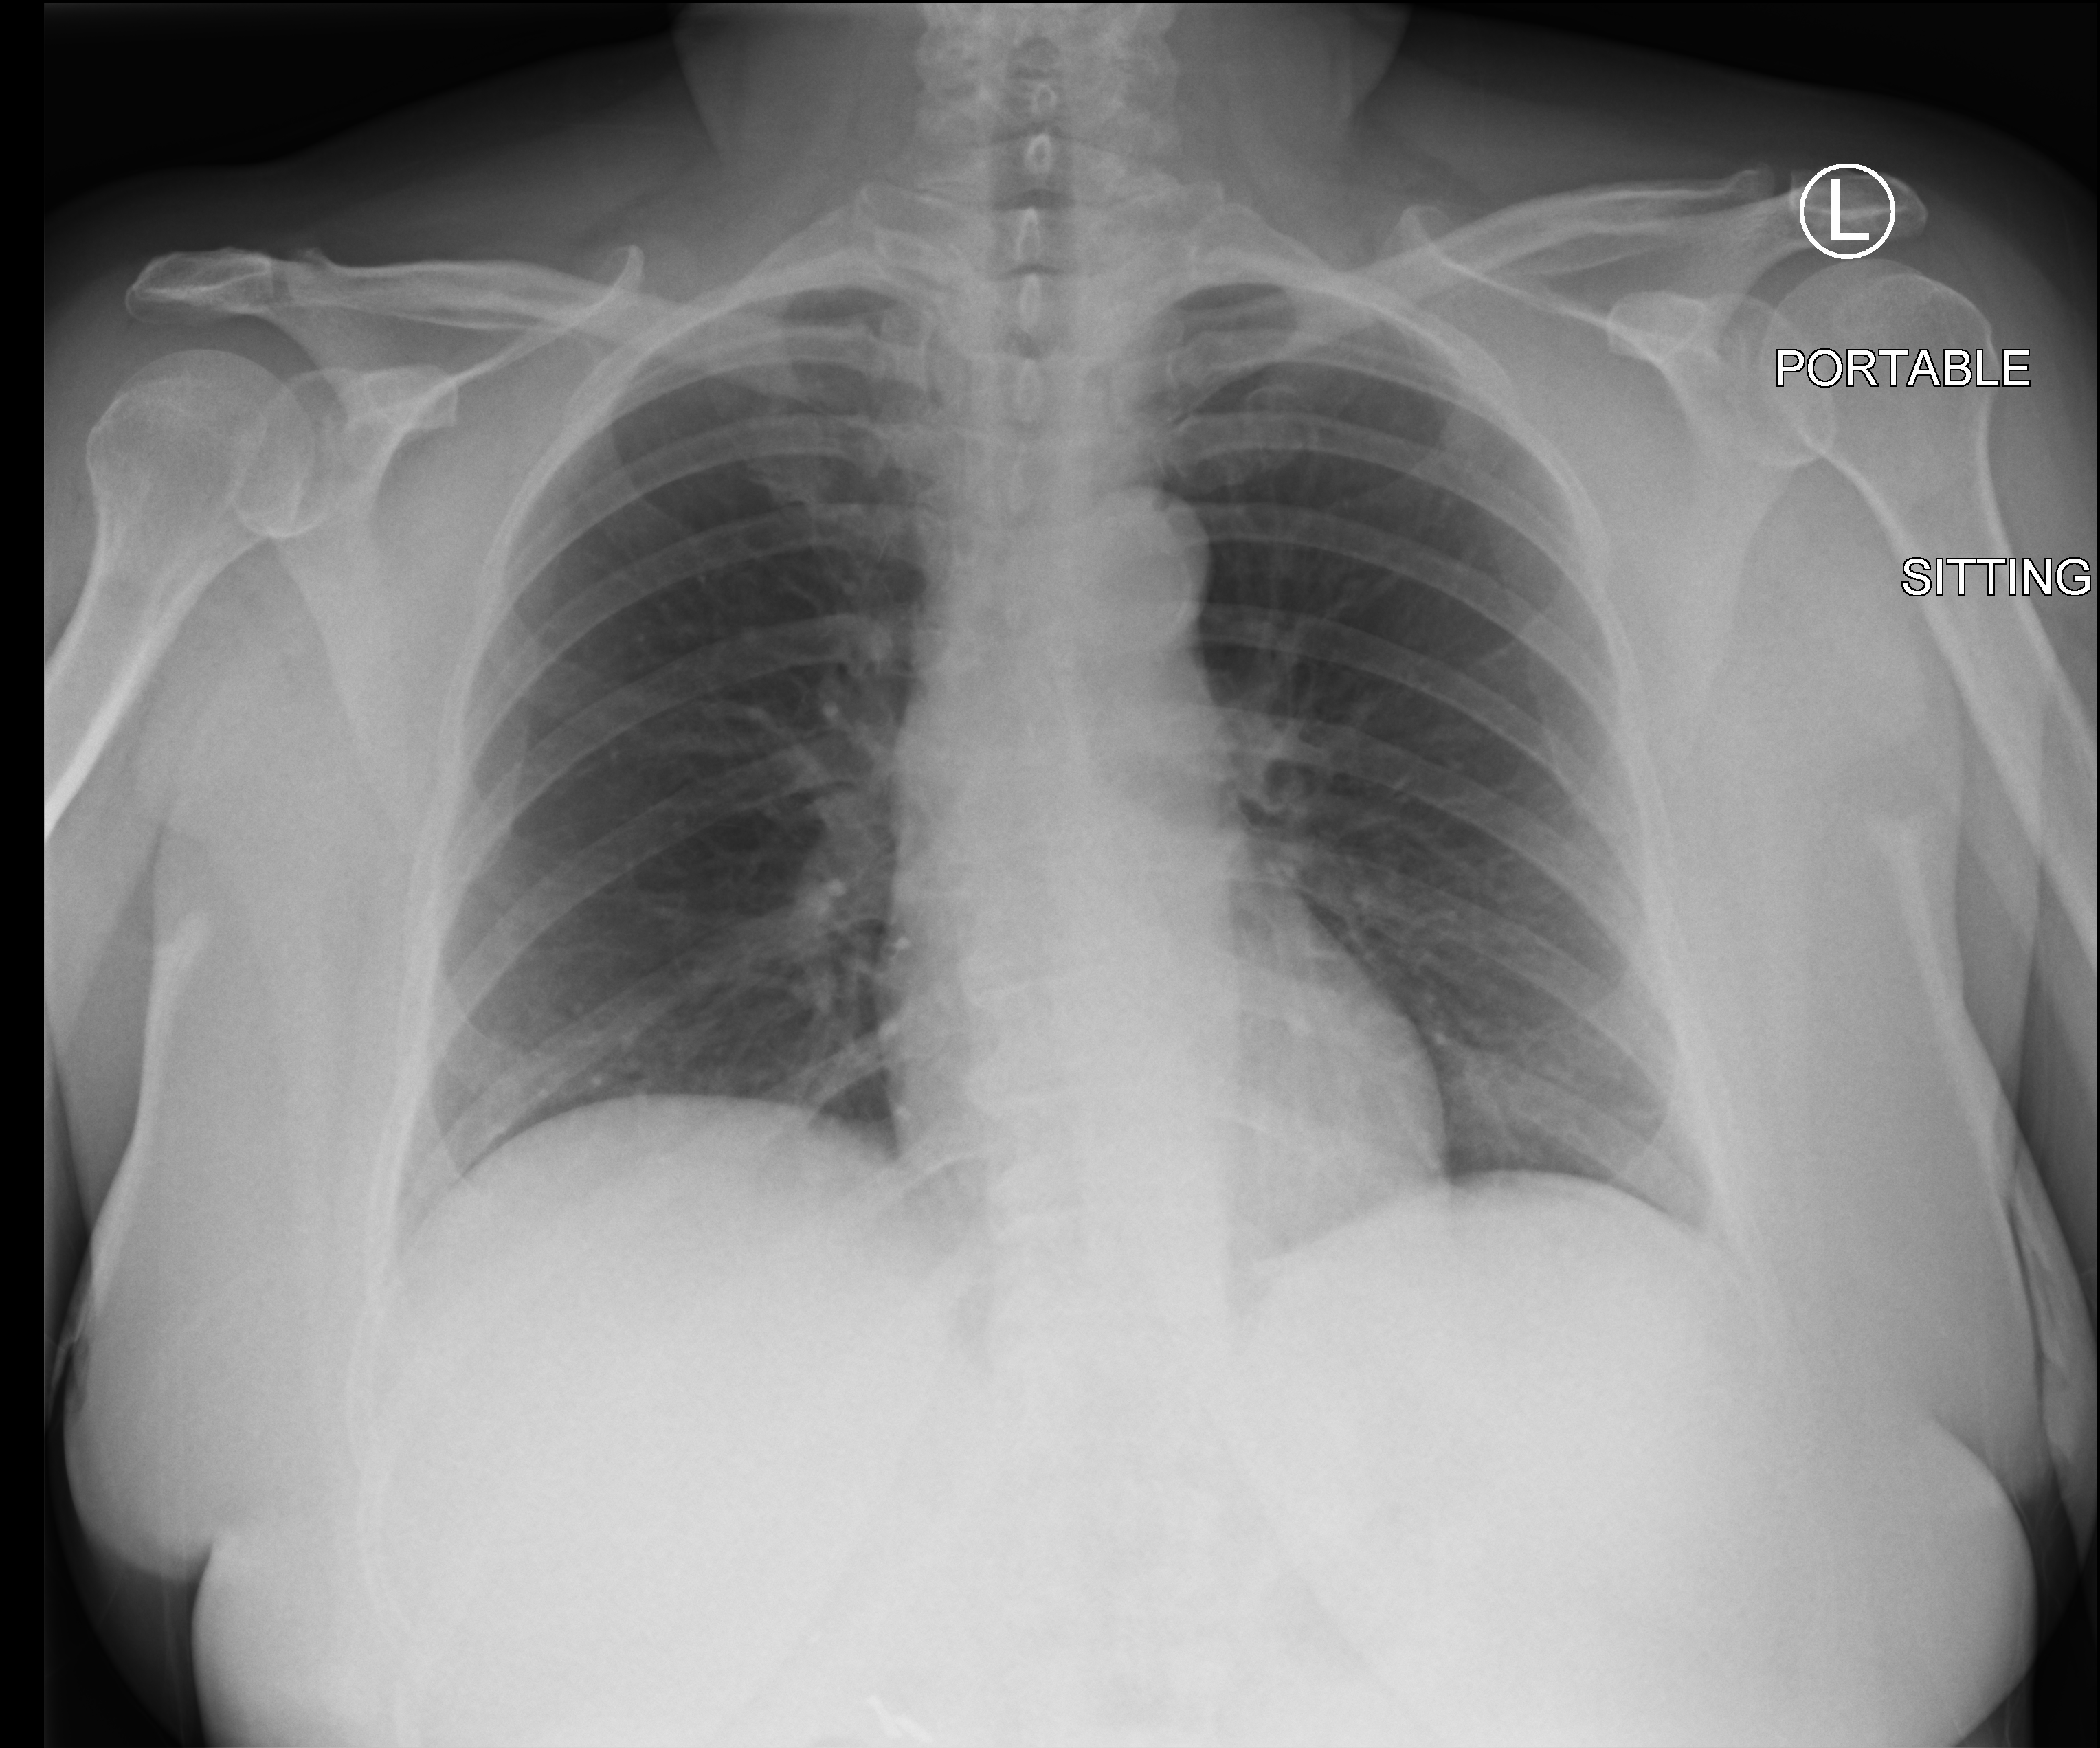
Portable chest radiograph; anteroposterior (AP) projection. Patient hospitalised with COVID-19; female, aged 60–74 years.
Admission-level facts for this patient (not findings on this image; timing relative to this image not recorded):
- mechanically ventilated during this hospital stay: no
- diabetes (admission record): no
- admitted to intensive care during this hospital stay: no